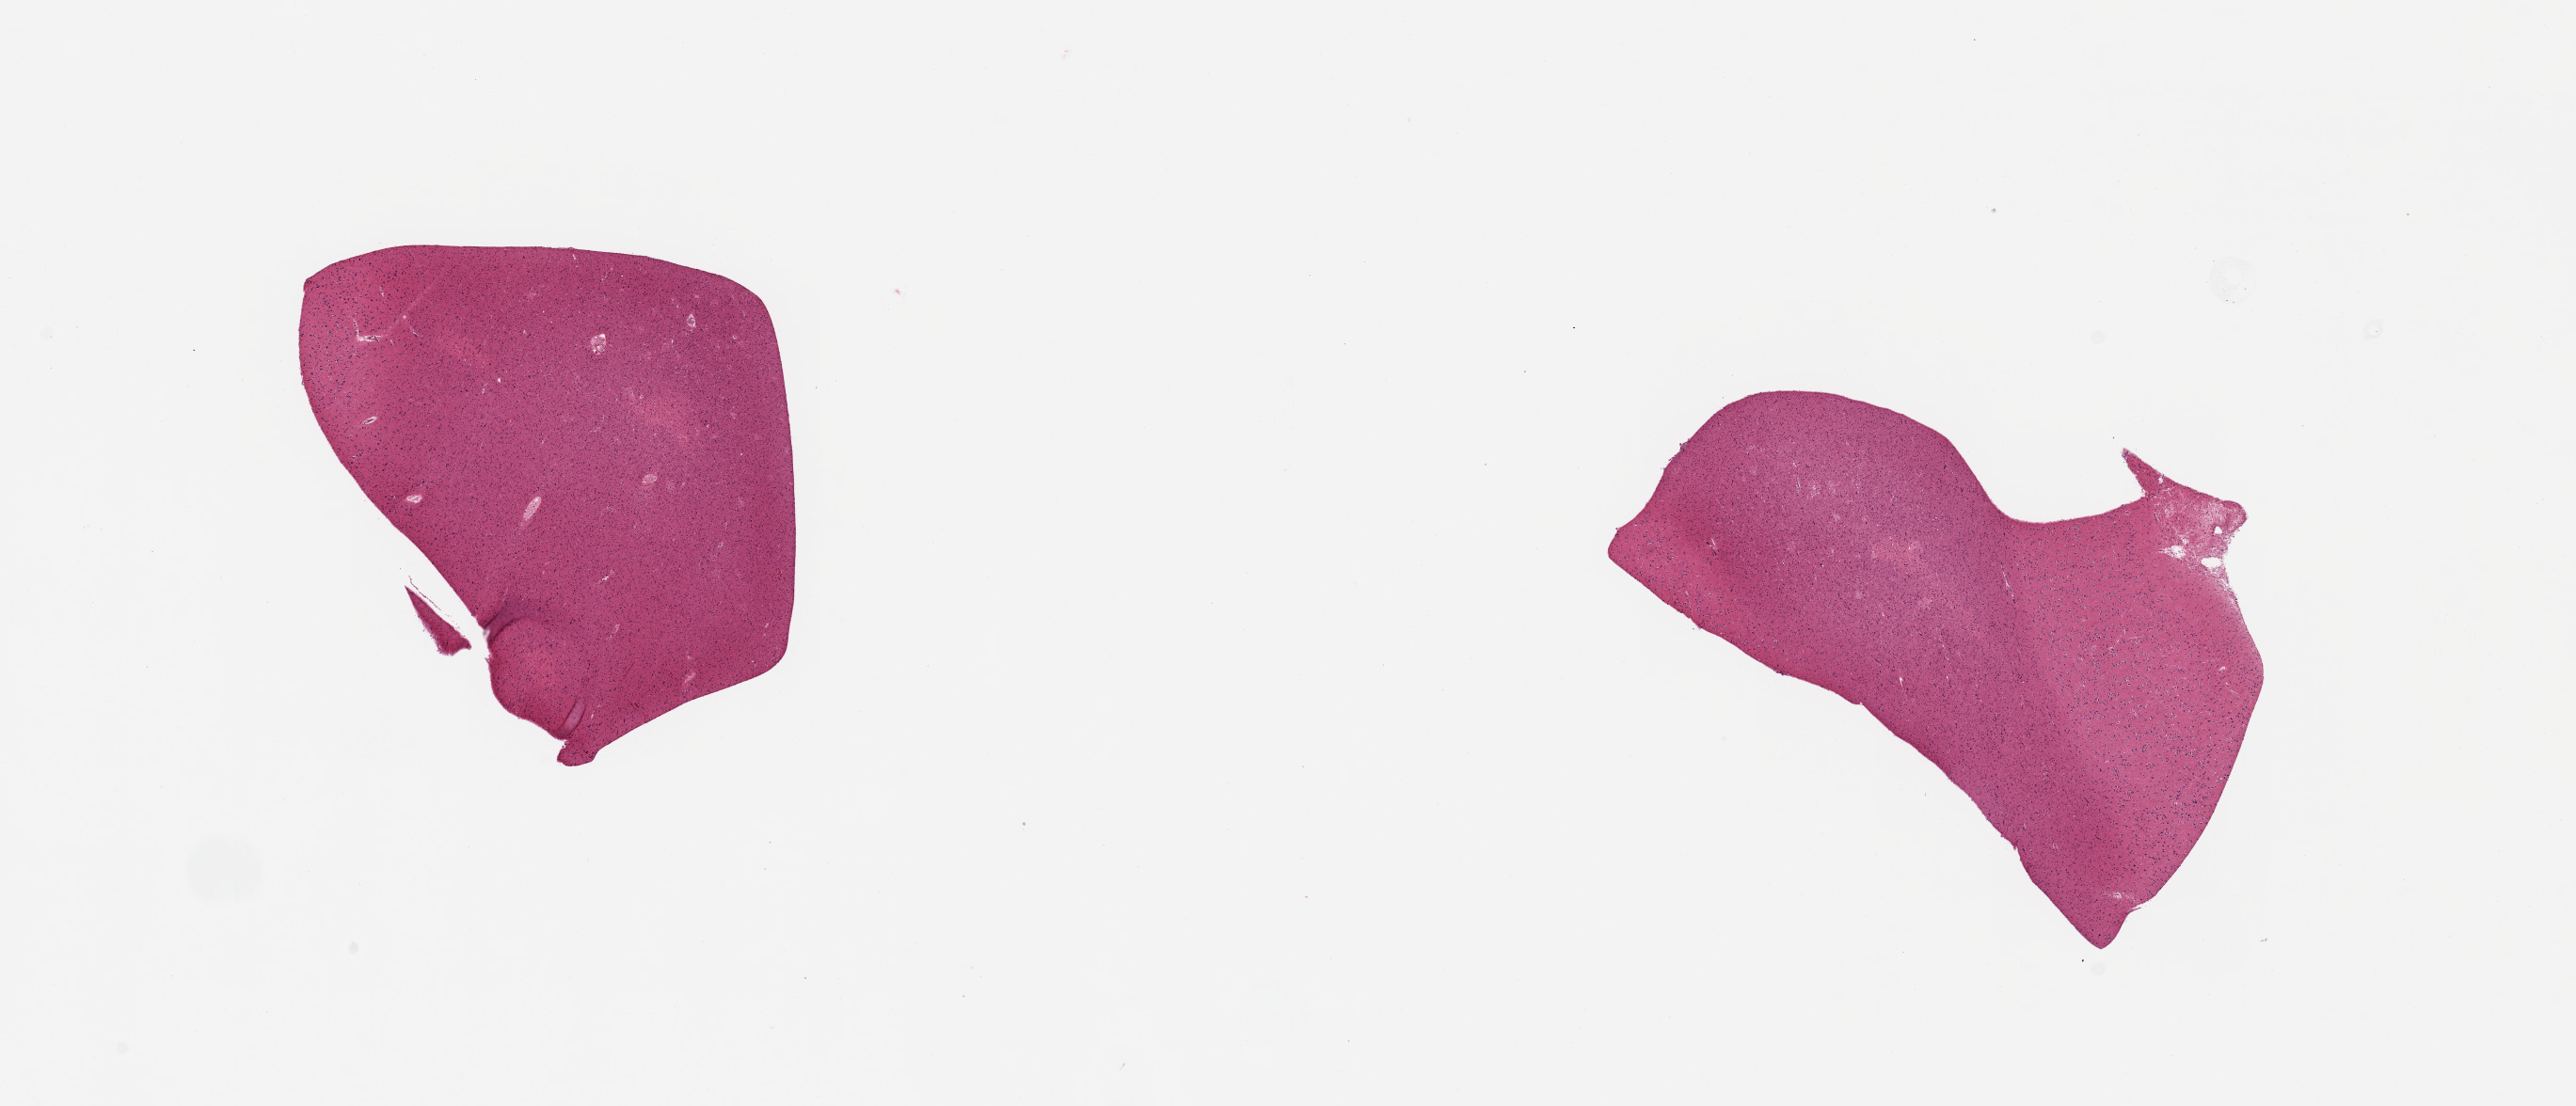
Digitized H&E-stained section — low-resolution overview of the scanned area, about 21.7 x 9.3 mm, PAXgene-fixed paraffin-embedded (PFPE) section, section of cerebral cortex (target tissue), tissue donor sample. Donor sex: female.
Review note (as recorded): 2 pieces.